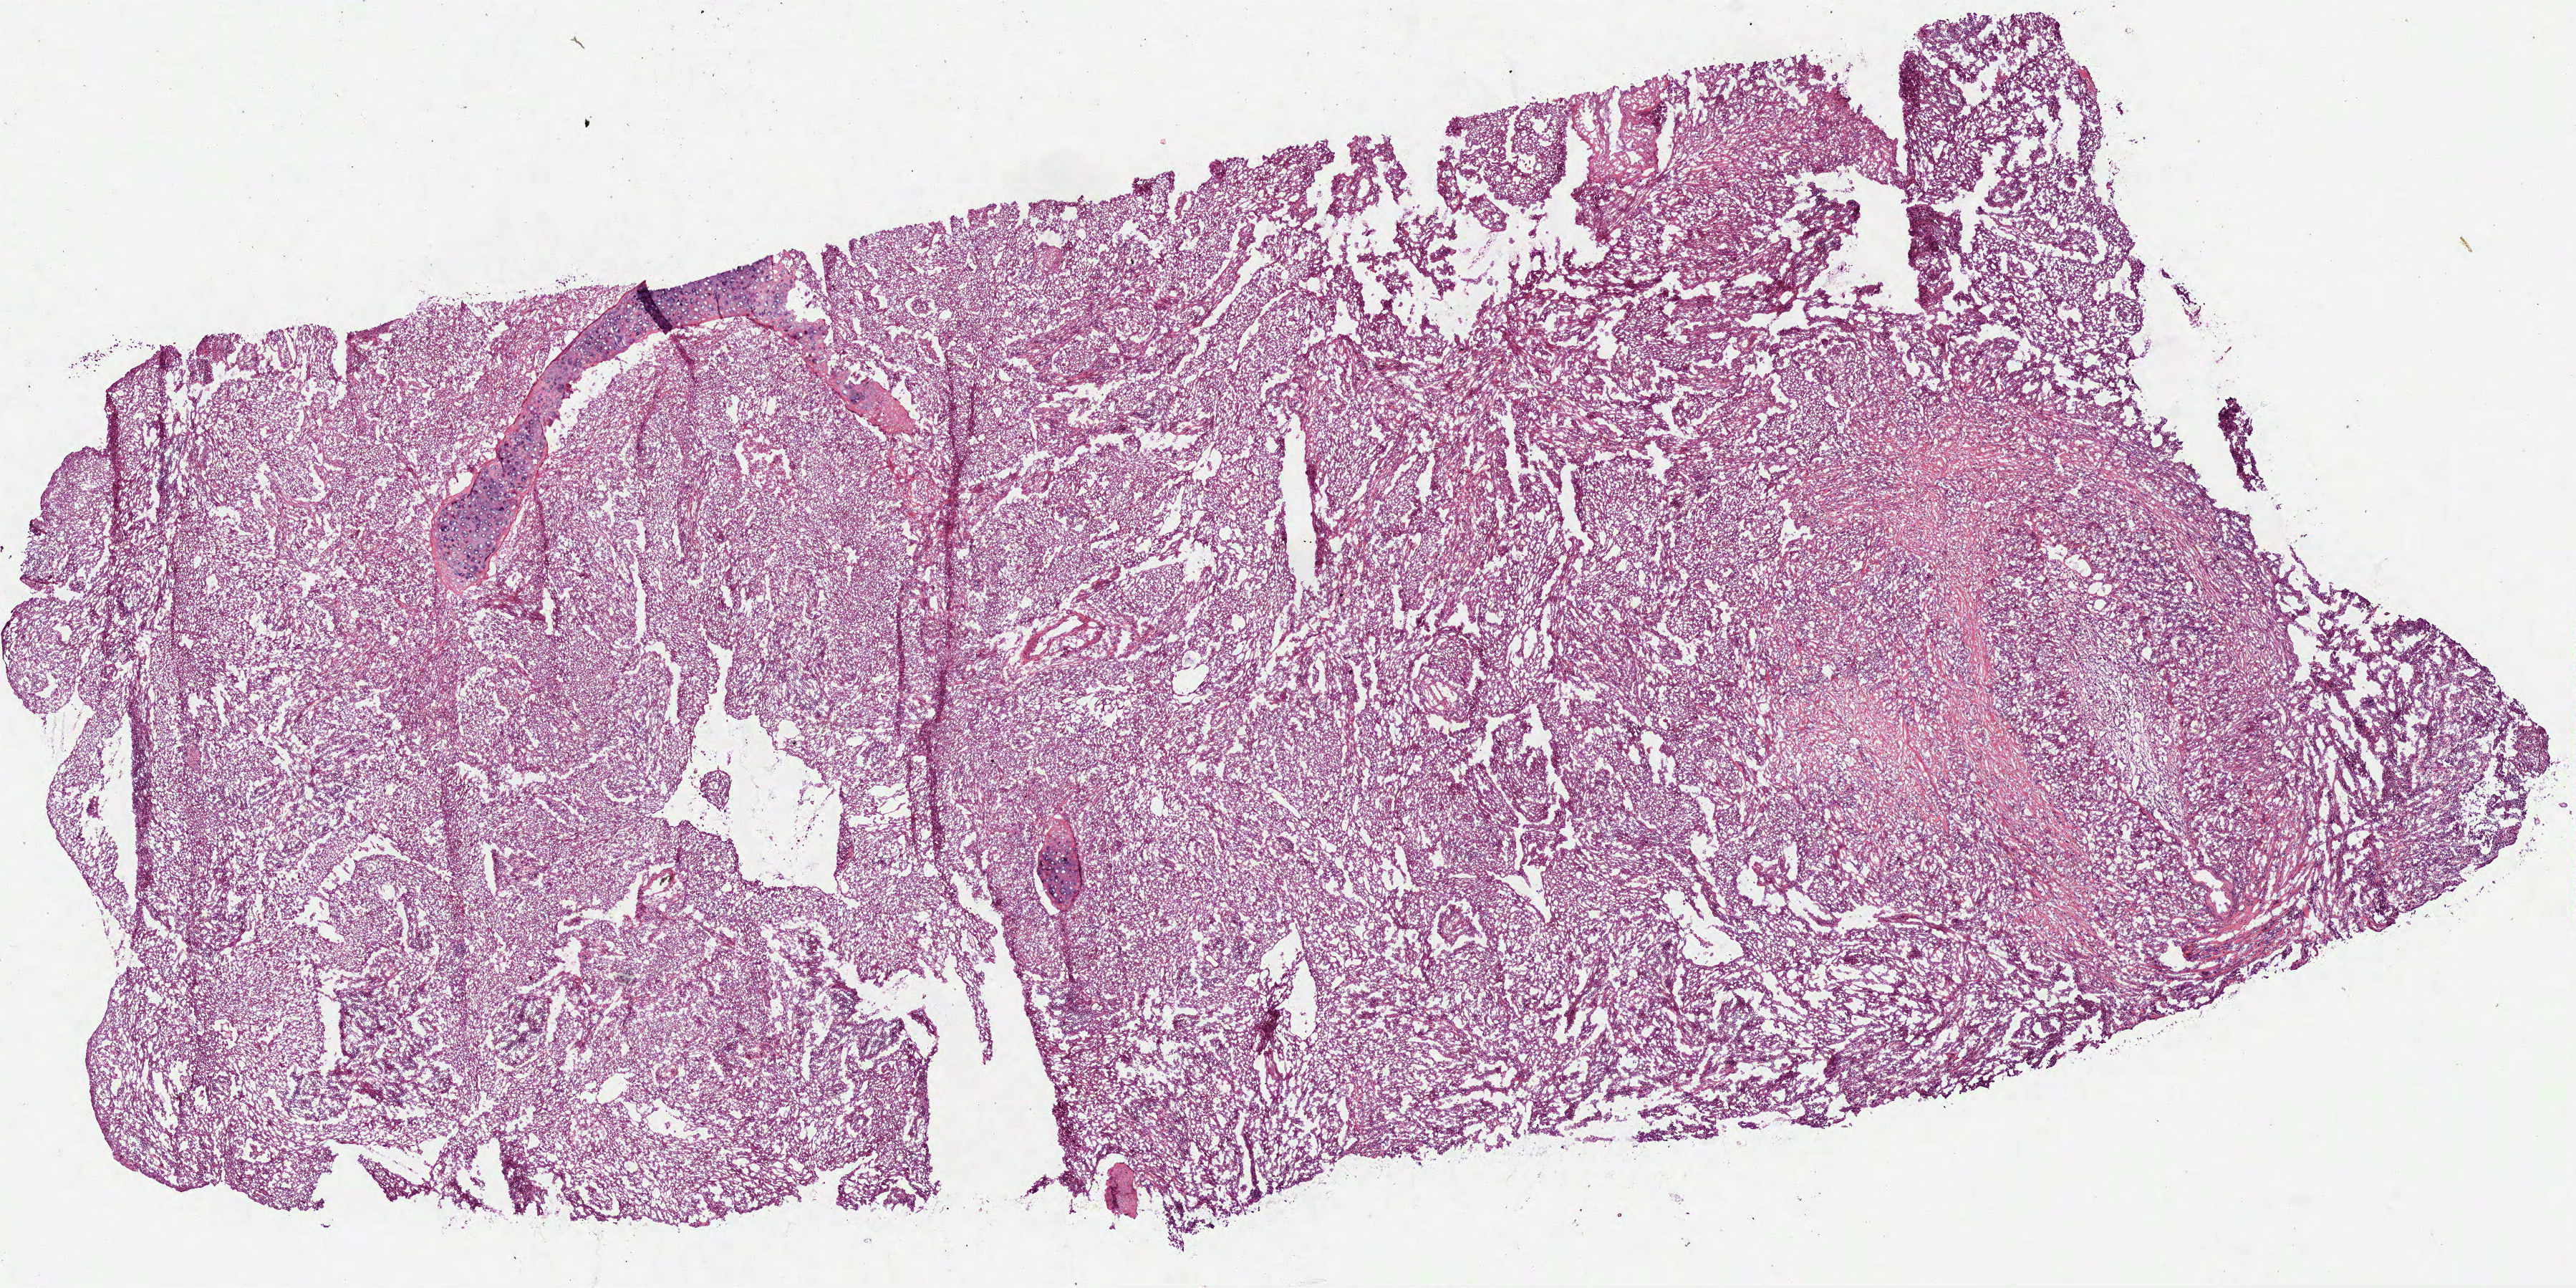
Digitized Hematoxylin and eosin (H&E) stained tissue section (whole slide), low-resolution overview of the scanned area, about 14.5 x 7.2 mm. Frozen section from the bottom of the tissue portion. Sample: primary tumour, lung. Female patient; age at initial diagnosis 46 years. Slide review estimates, as recorded: tumour cells 99%, tumour nuclei 85%, normal cells 1%, stromal cells 0%, necrosis 0%. Infiltration values recorded for this section: lymphocyte infiltration 5%, monocyte infiltration 0%, neutrophil infiltration 0%.
TNM: T3 N0 MX. Laterality: right. AJCC pathologic stage: IIB (7th edition). Diagnosis: Adenocarcinoma, NOS (middle lobe, lung).